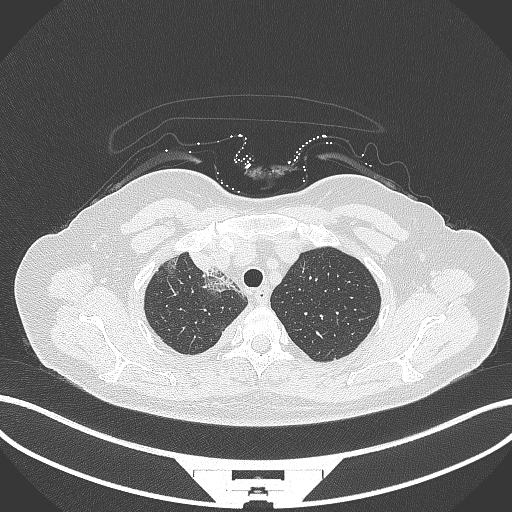
Chest CT, one axial slice; slice 261 of 305 in the series (ordered by position); 120 kVp; lung window (W 1500 / L -600 HU); 1 mm slice thickness; 512 × 512 image matrix, field of view 400 × 400 mm. Female patient, age 52 years. From the clinical record (not read from this slice): clinical TNM (as recorded): T3 N1 M1.
Outlined on this slice (rectangle marked by the reading radiologist):
- lung tumour (recorded histology: adenocarcinoma): bounding box [x1, y1, x2, y2] px = [183, 248, 220, 278]